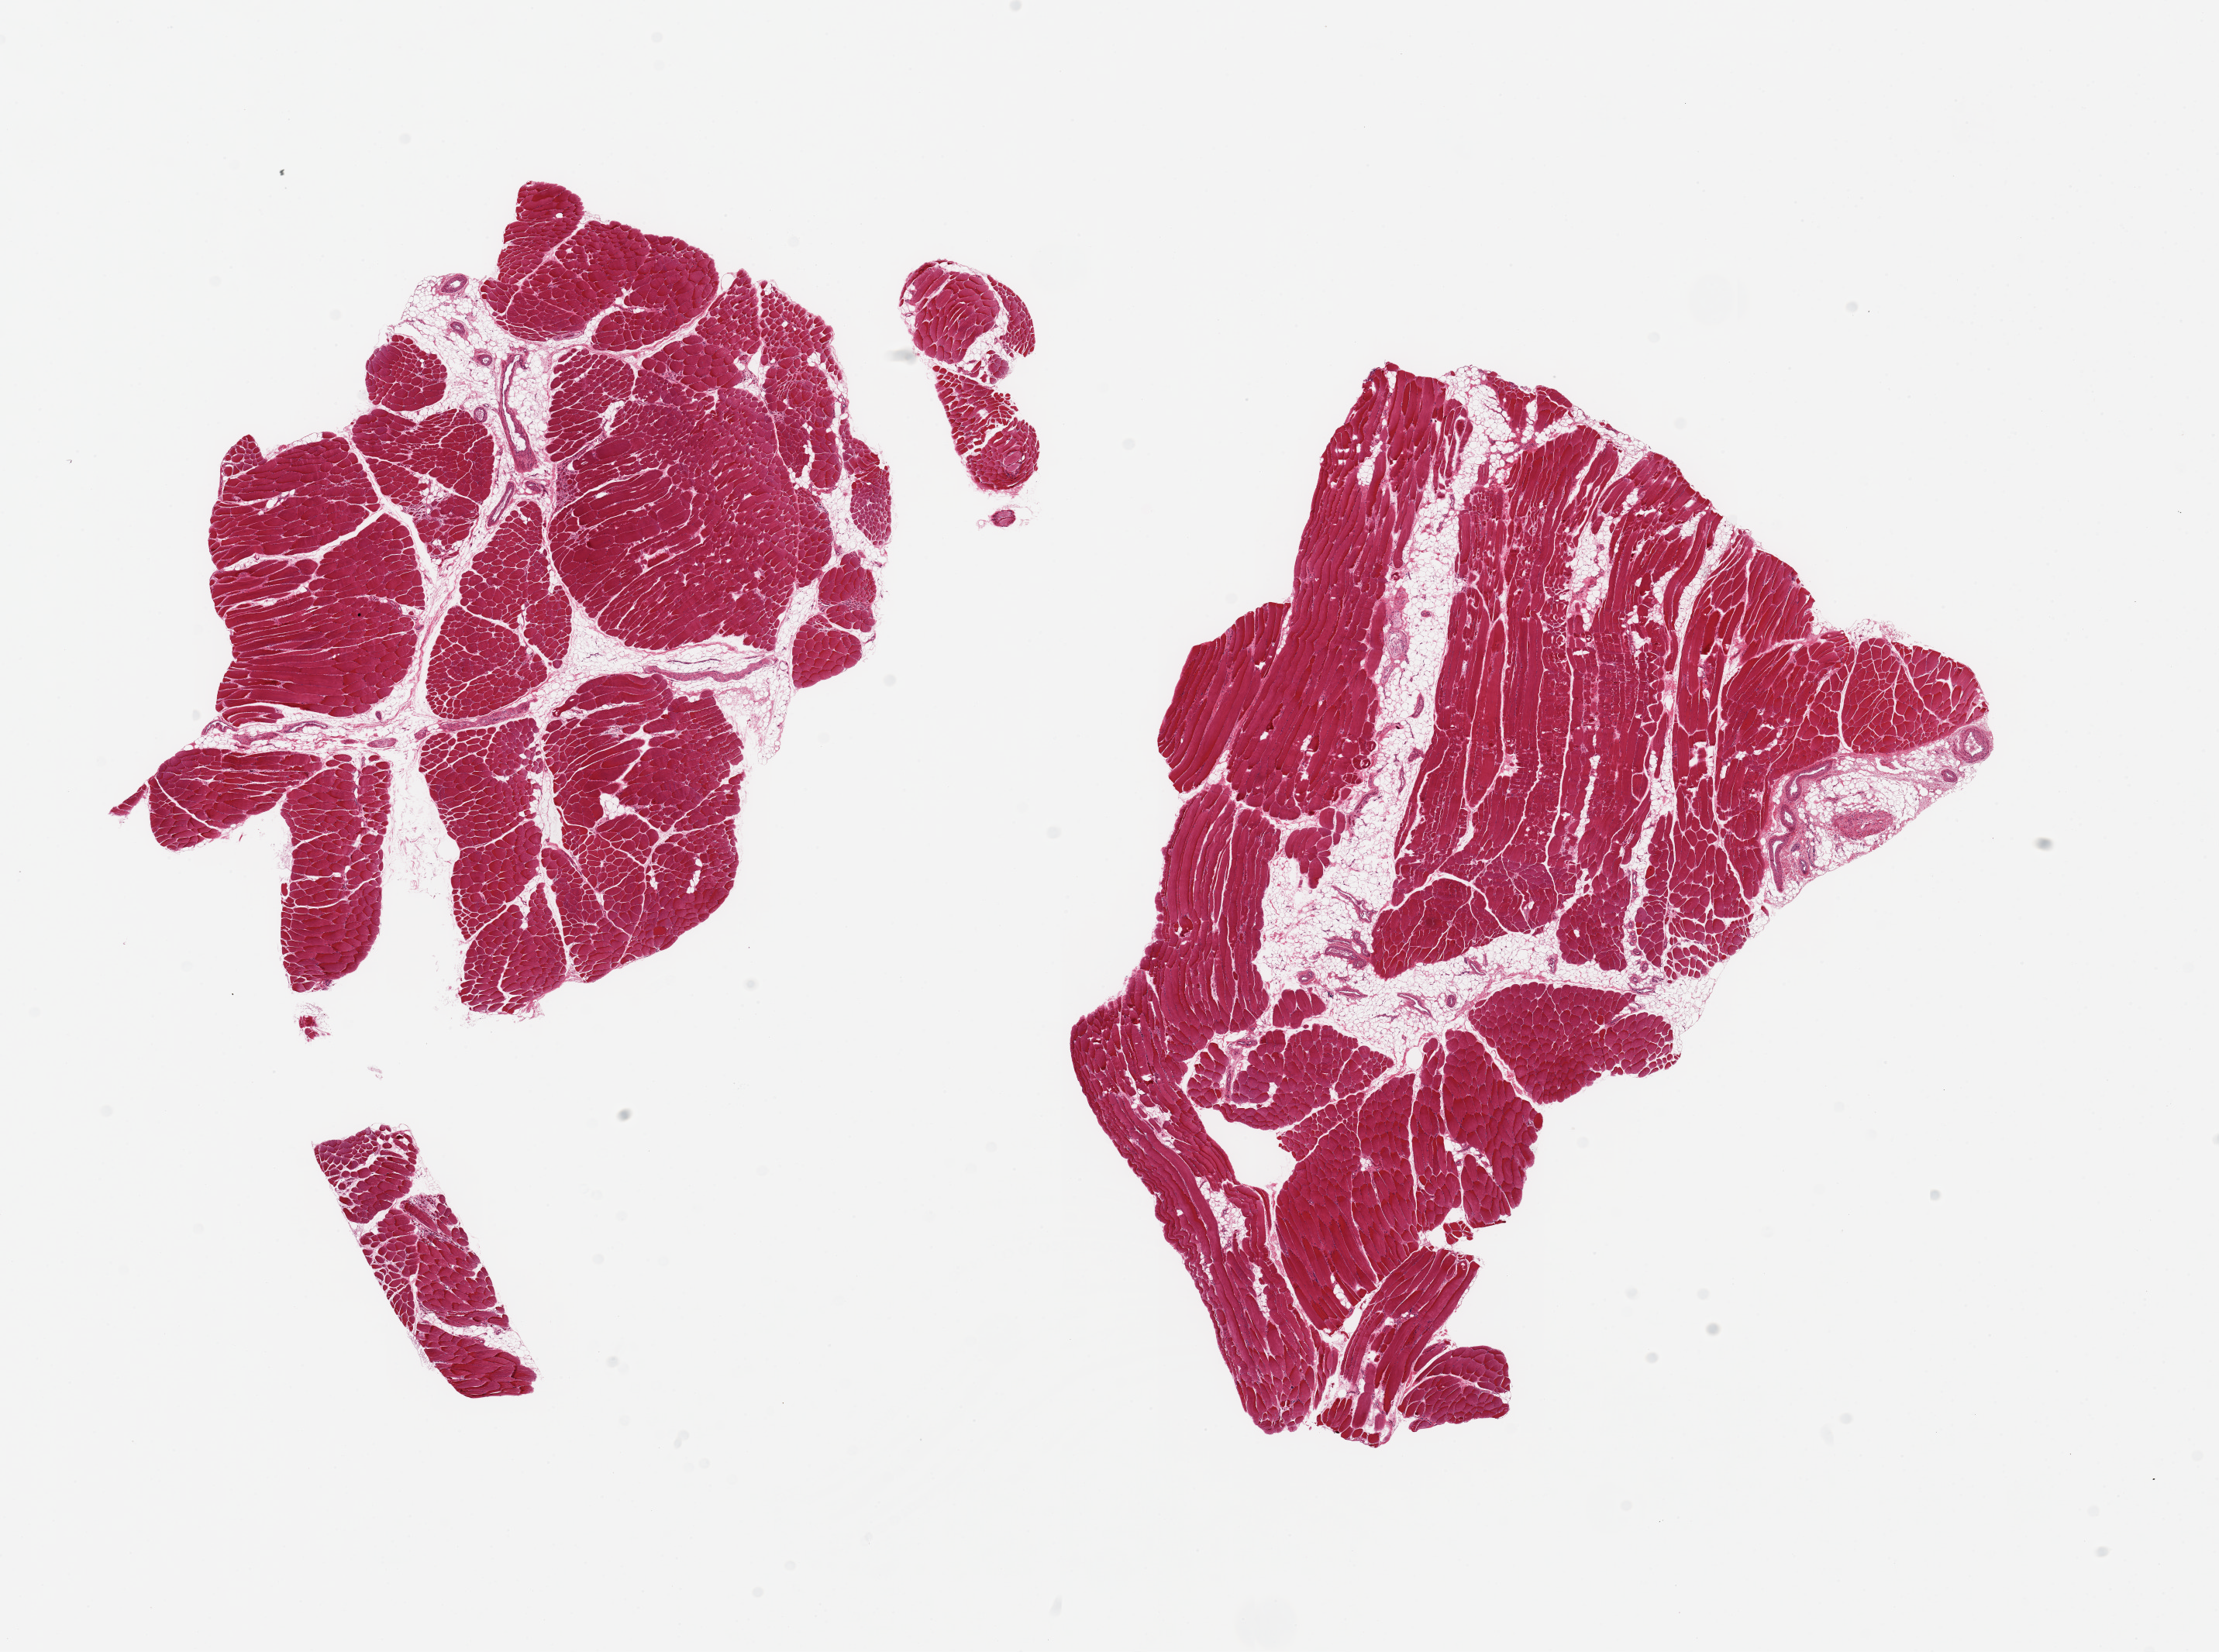
Whole-slide image, hematoxylin and eosin (H&E) stain — whole scanned area (about 22.6 x 16.9 mm) shown as a low-resolution overview; PAXgene-fixed, paraffin-embedded tissue; section of skeletal muscle (target tissue); donor tissue sample.
Review note (as recorded): 2 pieces; 10% internal fat.